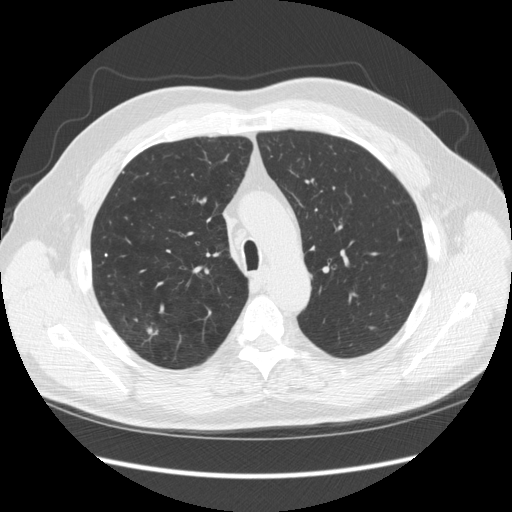
Chest CT (low-dose screening protocol), one axial image, third annual screen, lung window (W 1500 / L -600 HU), 2.5 mm slice thickness. Male participant, aged 64 years at enrolment. Former smoker at enrolment.
Expert reader's lesion annotation, box from (x=116, y=314) to (x=171, y=359) px. The screening reader recorded 4 non-calcified nodules or masses ≥4 mm on this exam (right upper lobe, right upper lobe, right upper lobe, right upper lobe); which of them this box marks is not recorded. Lung cancer was diagnosed 15 days after this screen: adenocarcinoma, NOS, right upper lobe, moderately differentiated (G2), stage IA (AJCC 6th edition), 14 mm at pathology.